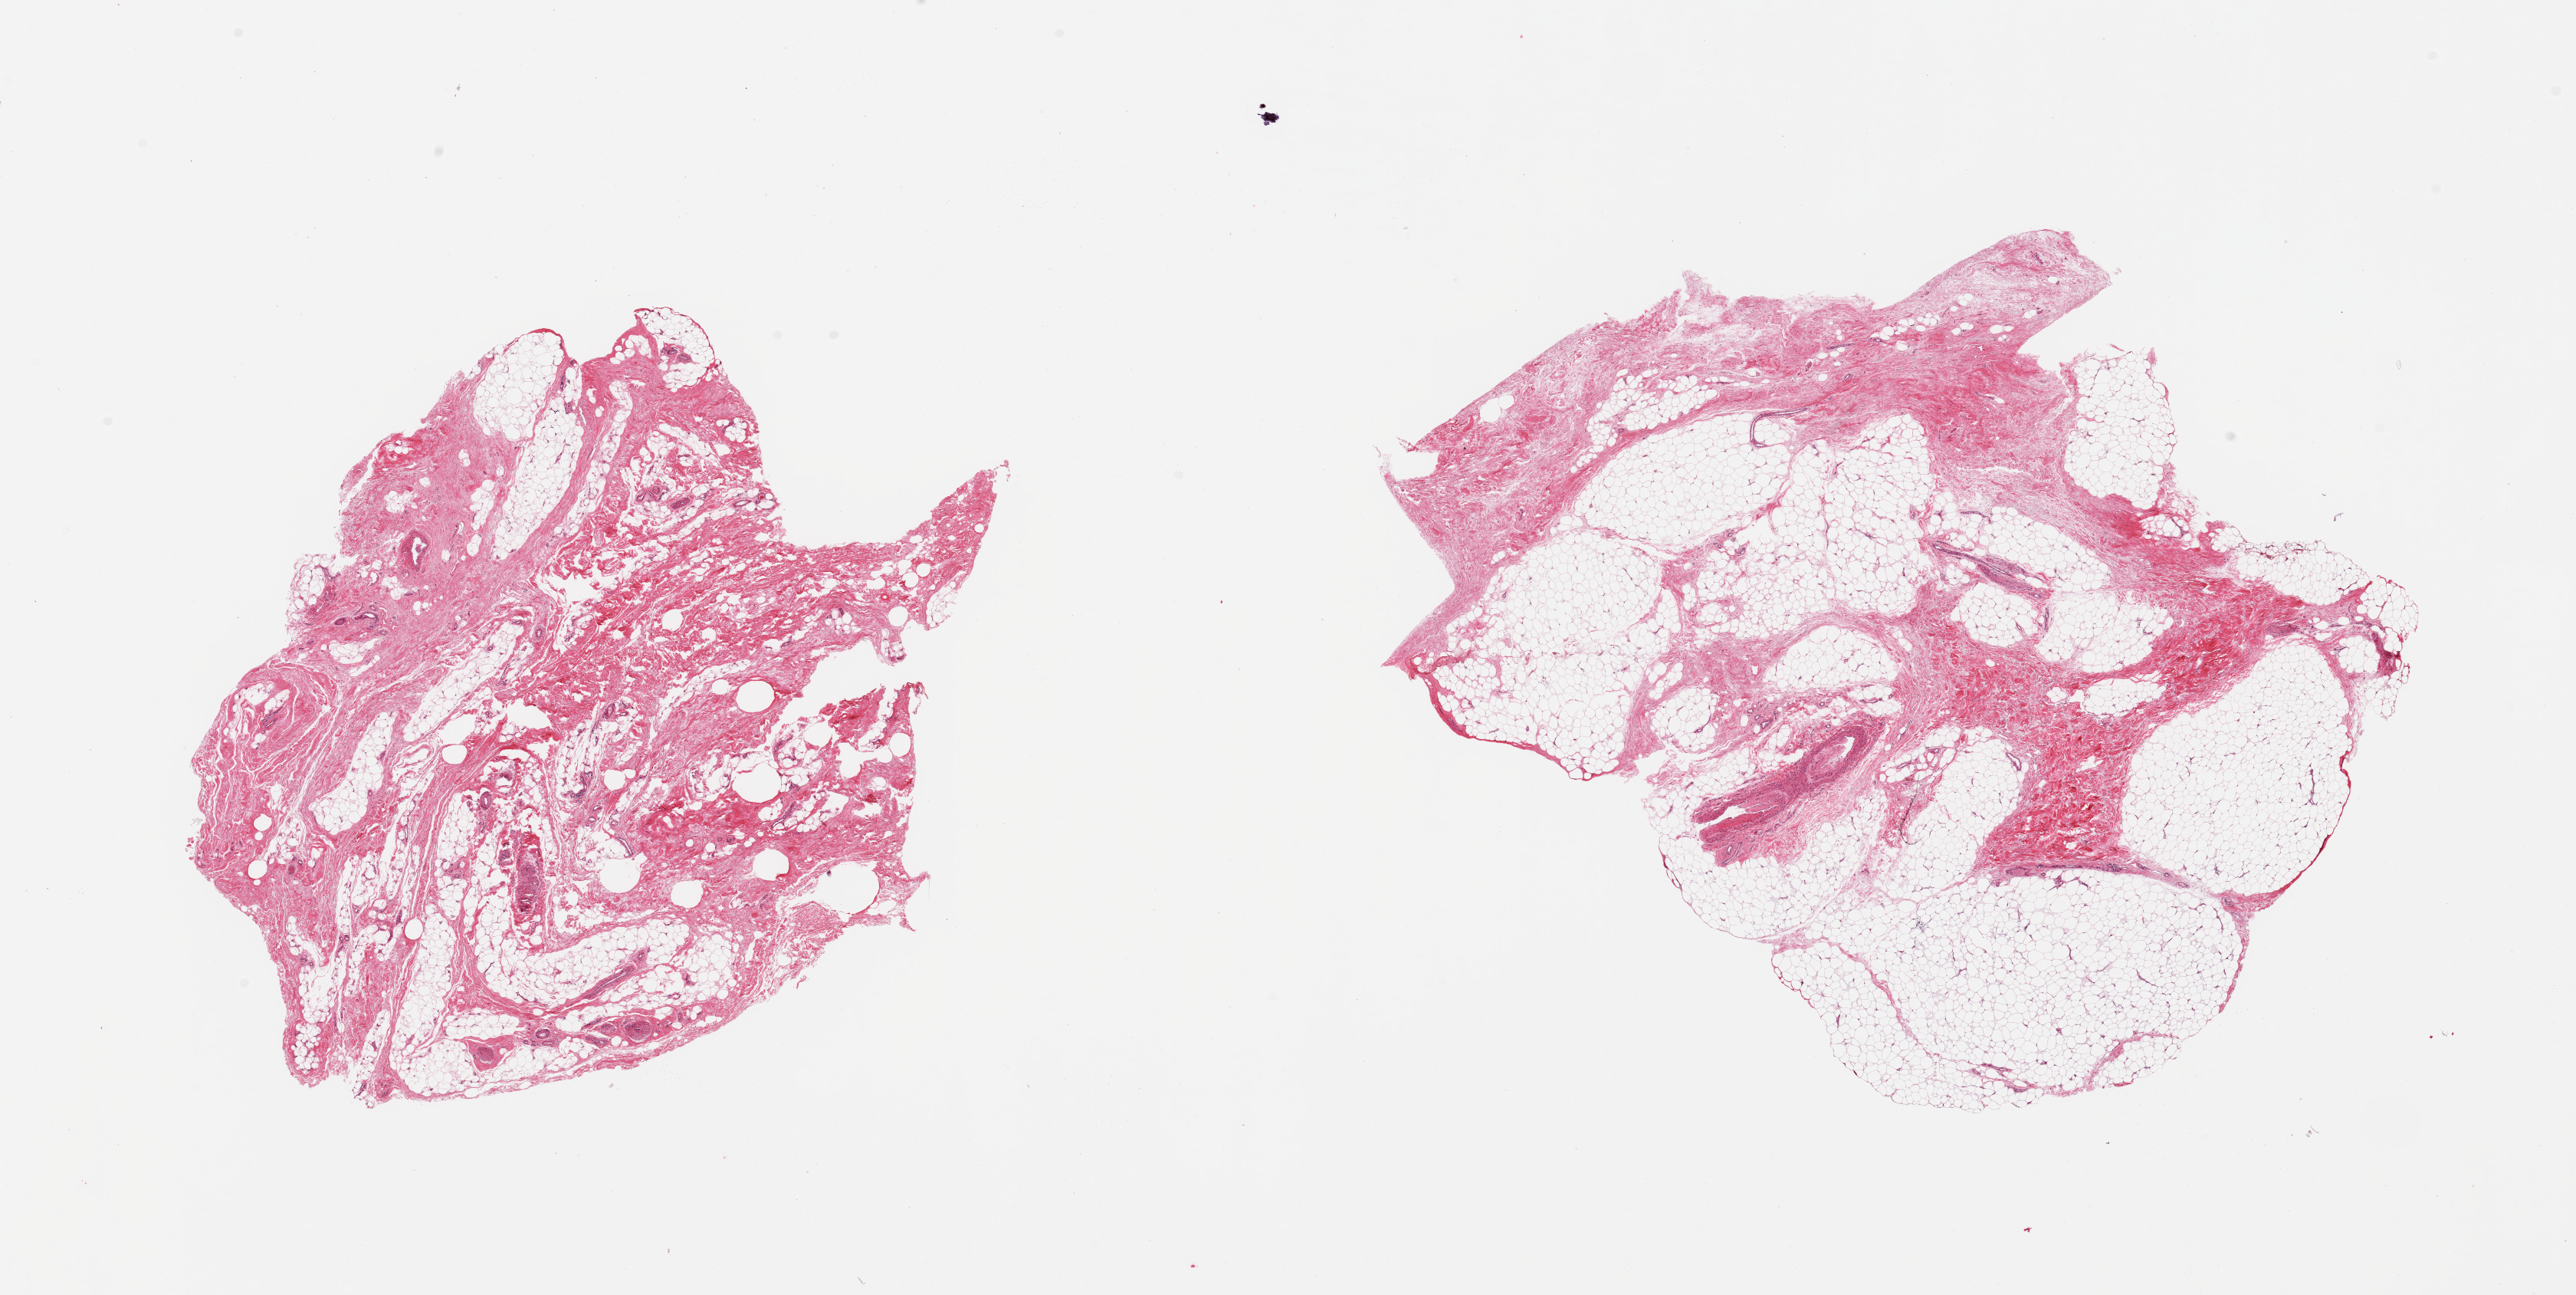
Haematoxylin and eosin whole-slide image, a low-resolution overview of the entire scanned area, about 26.6 x 13.4 mm (slide scanned at 20x). PAXgene-fixed, paraffin-embedded tissue. Target tissue: adipose tissue. Donor tissue sample. Donor sex: male.
Reviewer comment on this tissue sample: 2 pieces; 25 and 70% fat, remainder is fibrous/vascular/nerve.